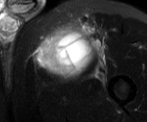
MRI of an extremity soft-tissue mass, one axial slice; slice 47 of 52 in the series (ordered by position); T2-weighted fat-saturated; MR volume resampled by the dataset authors to the PET/CT grid (not the native acquisition matrix); 3.27 mm slice thickness; 147 × 122 image matrix, field of view 144 × 119 mm. Male patient. Case-level facts recorded for this patient, not image findings: histological type: pleiomorphic liposarcoma; grade: high; site of the primary tumour: left thigh.
Annotated regions visible in this slice (expert contour drawn on MRI and transferred to this co-registered scan by the dataset authors):
- gross tumour volume including surrounding oedema: box from (x=39, y=23) to (x=104, y=76) px
- gross tumour volume (mass): (x=39, y=32)–(x=86, y=70)